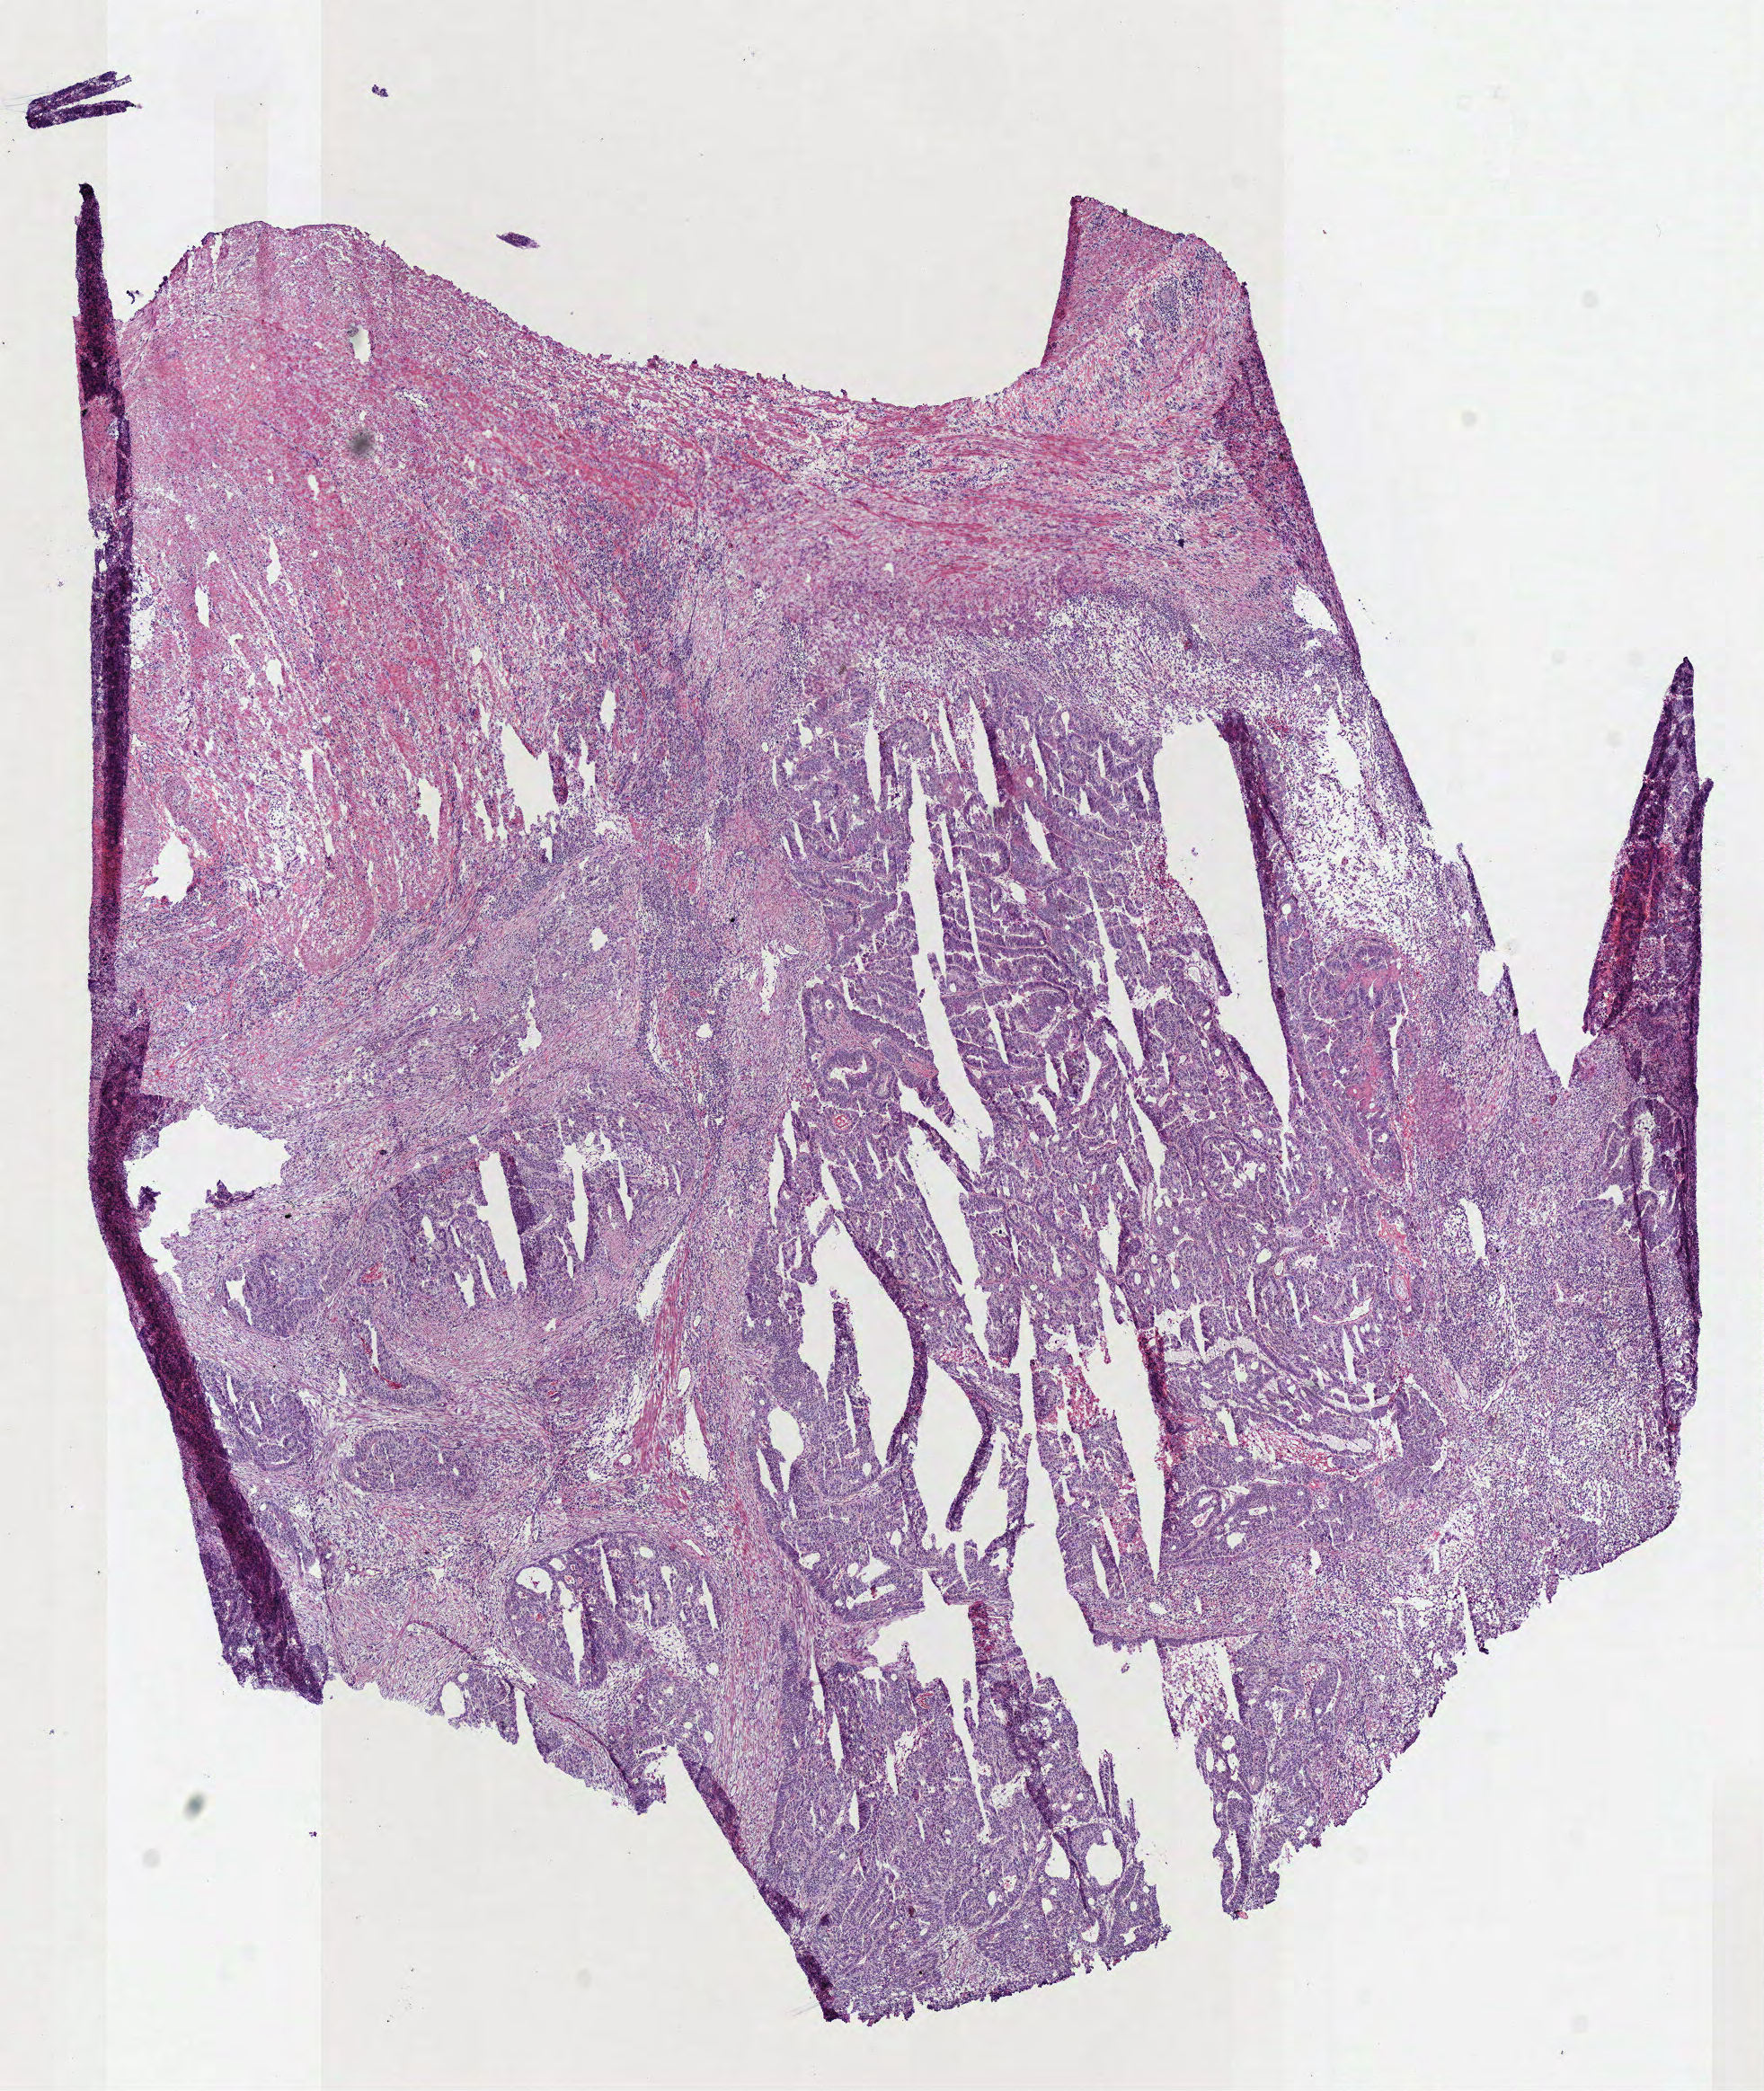
Digitized H&E-stained tissue section (whole slide), shown as a low-resolution overview of the whole scanned area (about 7.7 x 9.2 mm, from a 40x scan); frozen section; sample: primary tumour, colon. Male patient; age at initial diagnosis 68 years. Pathologist review of this section (percent, as recorded): tumour cells 25%, tumour nuclei 45%, normal cells 0%, stromal cells 74%, necrosis 1%. Infiltration values recorded for this section: lymphocyte infiltration 30%, monocyte infiltration 1%, neutrophil infiltration 2%.
• AJCC pathologic stage: IIA (7th edition)
• lymph nodes positive (case pathology): 0 of 8 examined
• histologic diagnosis: Adenocarcinoma, NOS (sigmoid colon)